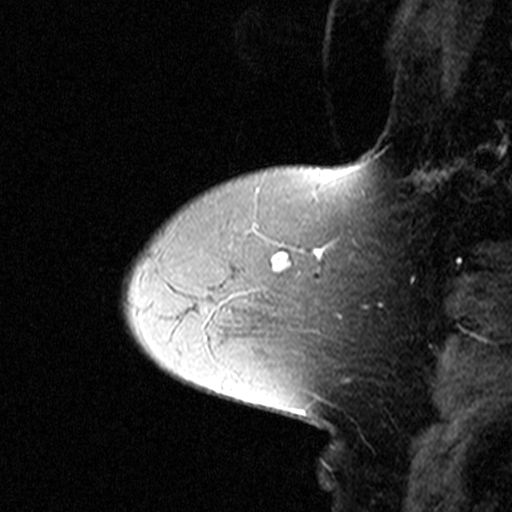
Breast MRI (dynamic contrast-enhanced), one sagittal slice. Slice 10 of 44 in the series (ordered by position). Dynamic contrast-enhanced study with each time point stored as its own series, time point 2 of 3 at this slice position (early post-contrast, ordered by acquisition time). 1.5 T. TE 4.5 ms, TR 11 ms. 3 mm slice thickness. 512 × 512 image matrix, field of view 200 × 200 mm. Patient: female, 50 years. From the clinical record (not read from this slice): setting: breast cancer imaged before/during neoadjuvant chemotherapy; receptor status: HR-positive, HER2-negative.
Annotated regions visible in this slice (semi-automatic segmentation, software-assisted and operator-edited):
- analysis volume of interest (the breast-tissue region the enhancement analysis was run in; not a lesion): bounding box [x1, y1, x2, y2] px = [180, 198, 300, 311]
- tumour enhancement mask (voxels above the 90 % enhancement threshold inside the analysis volume of interest): [273, 253, 290, 272]